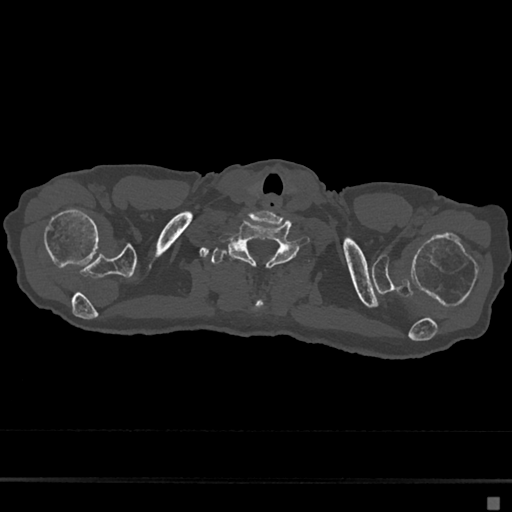
CT including the spine, one axial slice; position 632 of 797 along the scan axis; reconstruction kernel Br40s/3; bone window (W 1800 / L 400 HU); 0.5 mm slice thickness; 512 × 512 image matrix, field of view 360 × 360 mm. Patient: female, 68 years. From the clinical record (not read from this slice): primary cancer: renal.
Annotated regions visible in this slice (semi-automatically segmented with operator editing):
- T1 vertebra: bounding box (x1, y1, x2, y2) in pixels: (211, 245, 310, 311)